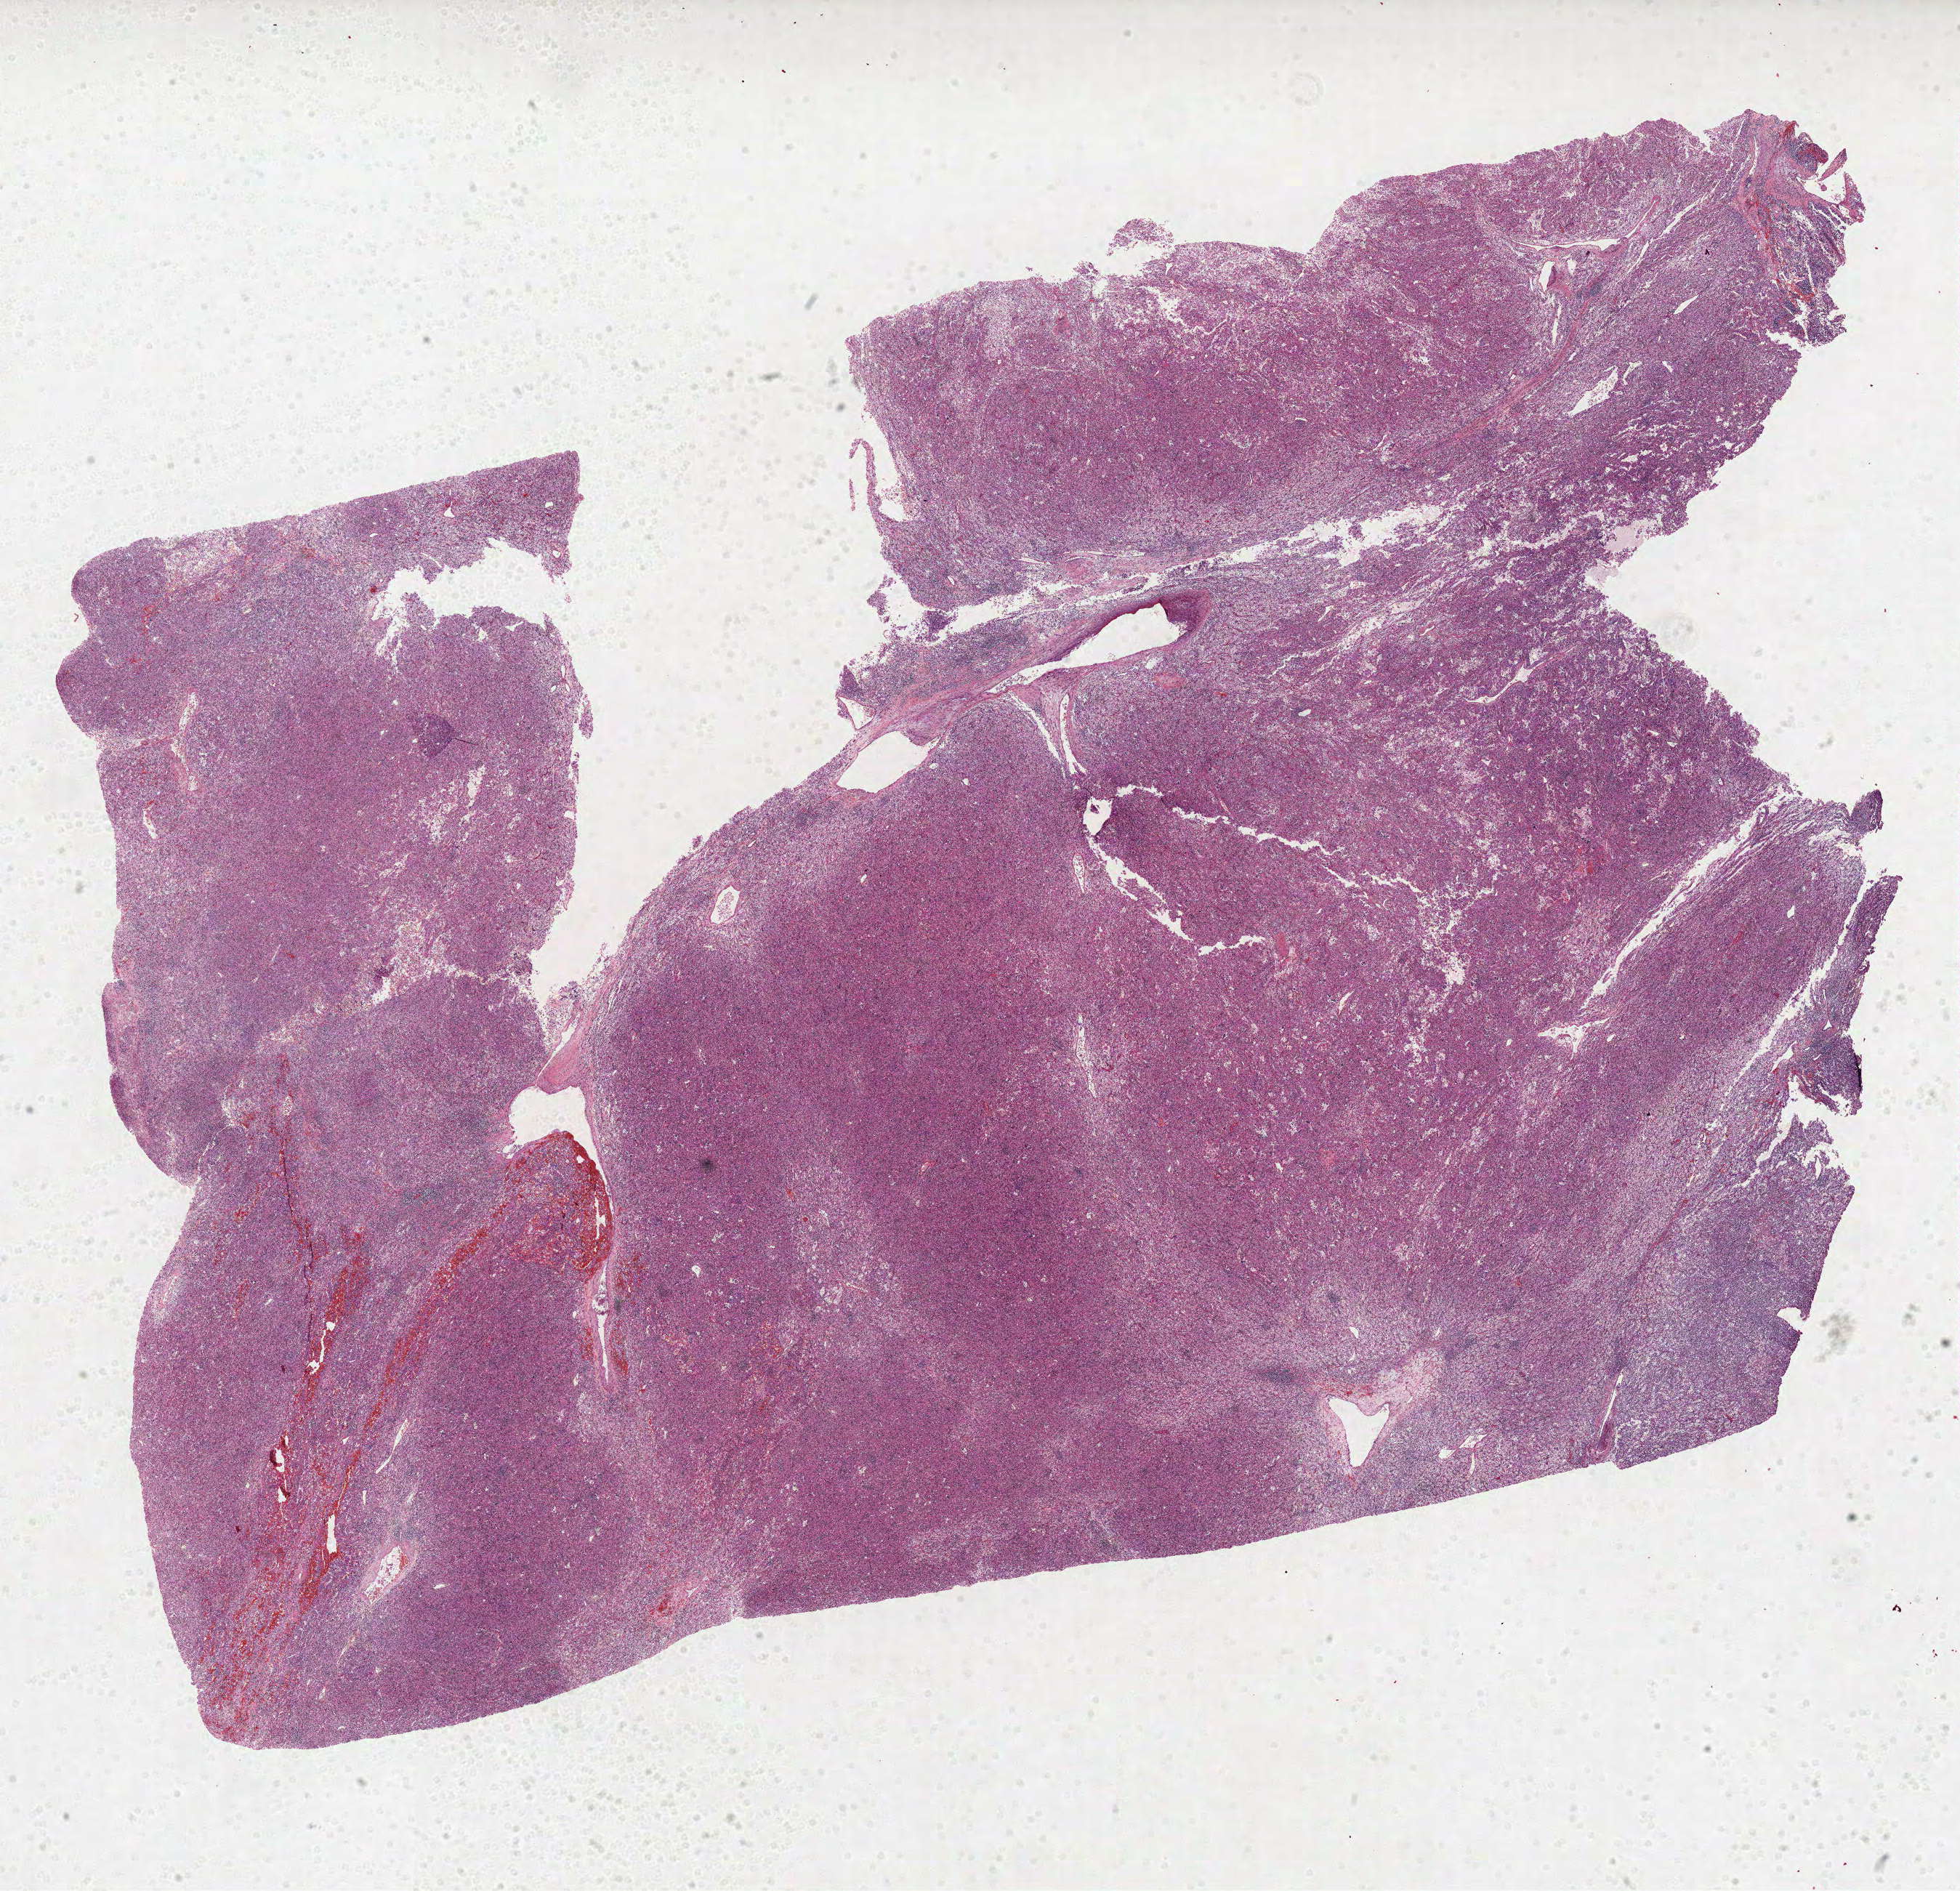
Whole-slide histology image, Hematoxylin and eosin (H&E) stained, low-resolution overview of the scanned area, about 21.8 x 21.0 mm, FFPE section, primary tumour sample from the kidney. Female patient; age at initial diagnosis 65 years. Histologic grade: G4 (undifferentiated).
- histologic diagnosis: Clear cell adenocarcinoma, NOS
- AJCC pathologic stage: IV